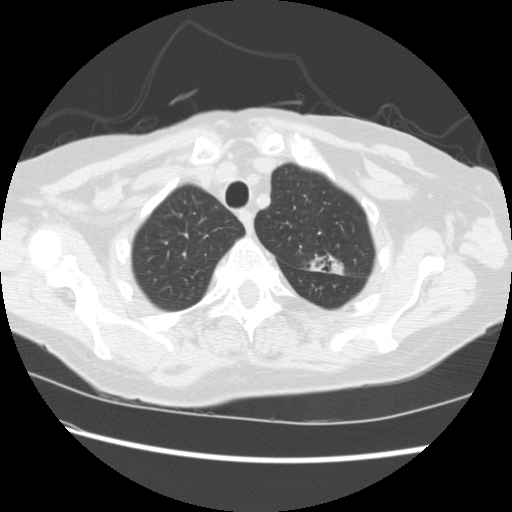
Low-dose screening chest CT, one axial slice. Position 185 of 224 along the scan axis. Lung window (W 1500 / L -600 HU). 512 × 512 image matrix, field of view 340 × 340 mm.
Outlined on this slice (expert manual segmentation):
- lesion 1 (tumor, upper lobe of left lung): bounding box <329,256,344,275> (left, top, right, bottom; pixels)